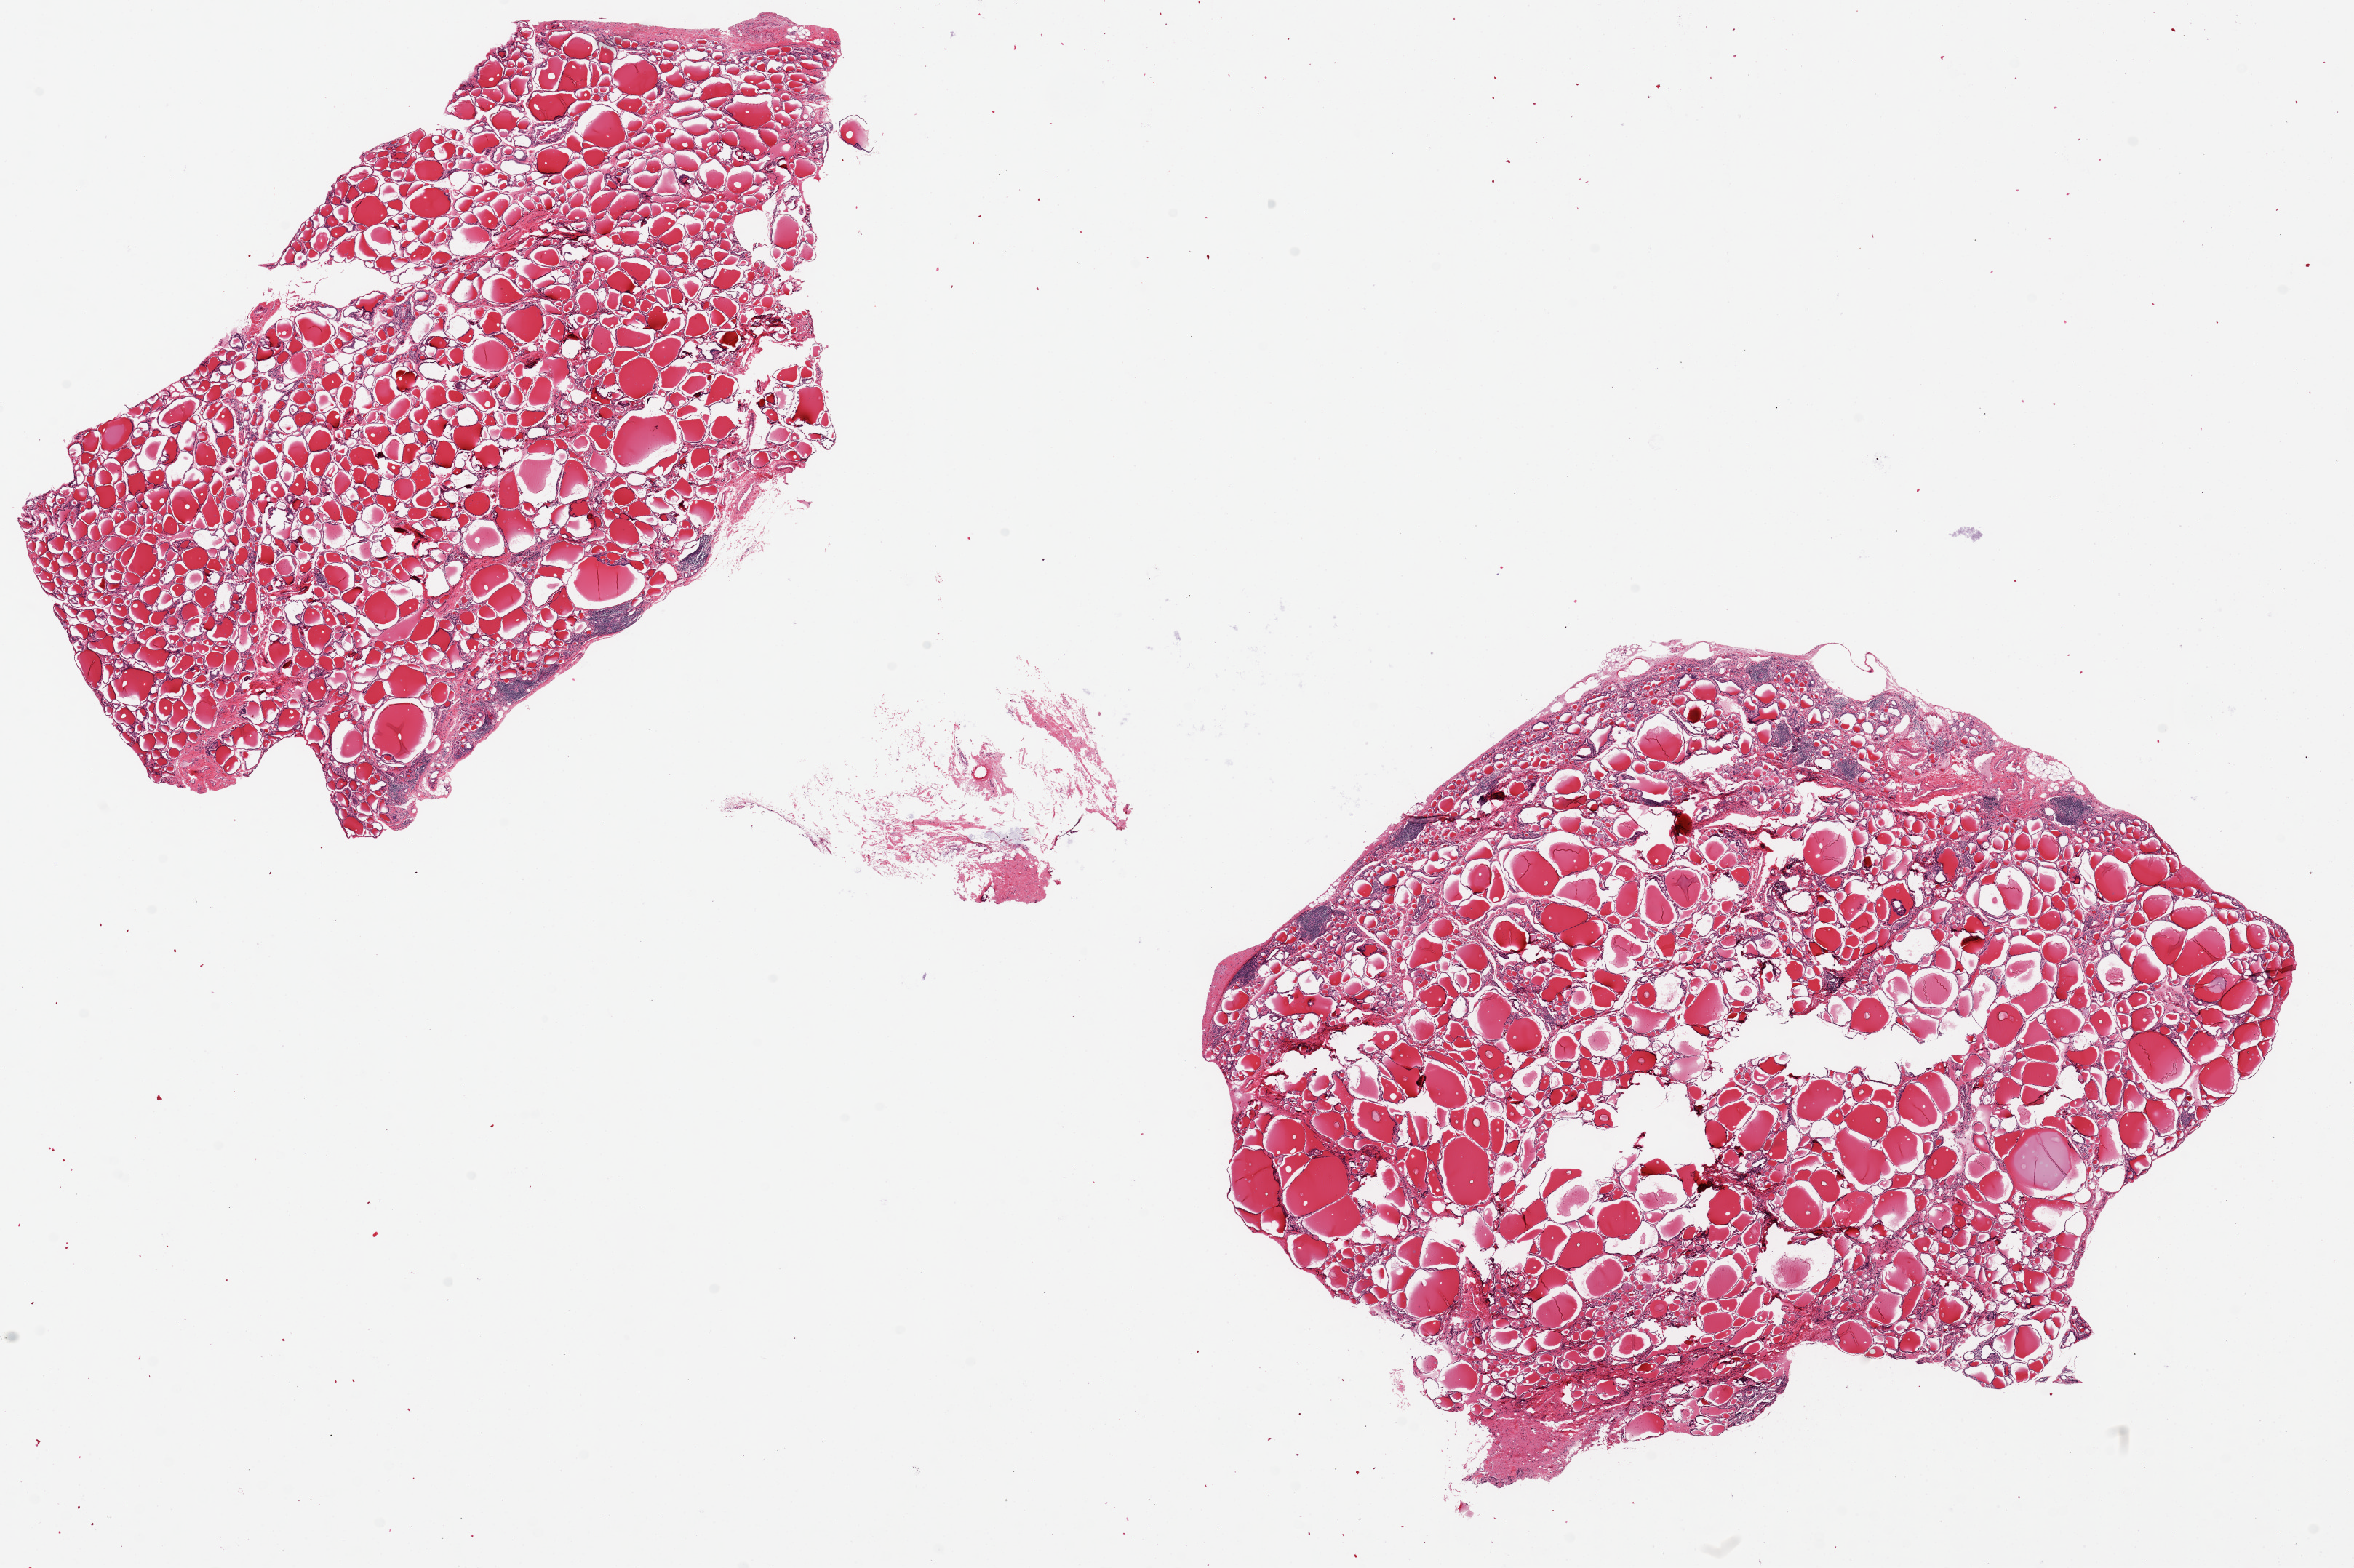
Whole-slide image, H&E stain, brightfield — low-resolution overview of the scanned area, about 25.6 x 17.1 mm; PAXgene-fixed paraffin-embedded (PFPE) section; section of thyroid (target tissue); donor tissue sample. Donor: female.
Review note (as recorded): 2 pieces, 11x6 & 12x9mm; pathcy areas lymphocytic or Hashimoto thyroiditis, ~10% specimens.